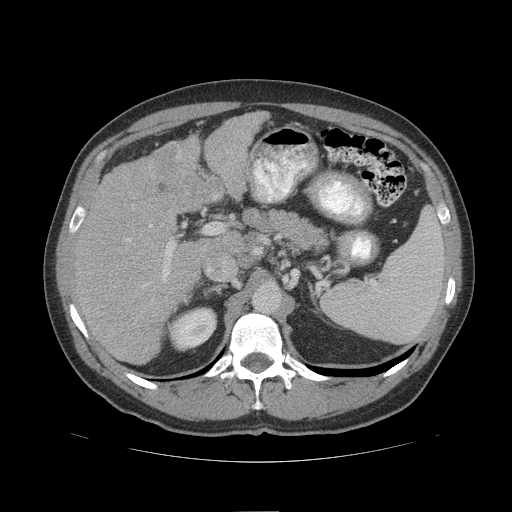
Contrast-enhanced abdominal CT (liver protocol), one axial slice. Reconstruction kernel STANDARD. Soft-tissue window (W 400 / L 40 HU). 2.5 mm slice thickness. 512 × 512 image matrix, field of view 420 × 420 mm. Case-level facts recorded for this patient, not image findings: diagnosis: hepatocellular carcinoma (patient treated with transarterial chemoembolisation; whether this scan precedes or follows treatment is not stated here); TNM stage (as recorded): Stage-IIIB; Child-Pugh class: A; tumour nodularity: multinodular.
Annotated regions visible in this slice (semi-automatic segmentation, software-assisted and operator-edited):
- liver parenchyma outside the tumour (the mass and vessels are separate outlines, so this box may not span the whole liver): bounding box [x1, y1, x2, y2] px = [74, 110, 268, 364]
- liver vessels: [149, 224, 211, 280]